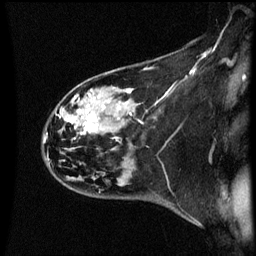
Breast MRI (dynamic contrast-enhanced), one sagittal slice; position 41 of 60 along the scan axis; dynamic contrast-enhanced series, image 2 of 3 at this slice position (ordered by acquisition); 1.5 T; TE 4.2 ms, TR 8.9 ms; 2 mm slice thickness; 256 × 256 image matrix. Female patient, age 44 years. Case-level facts recorded for this patient, not image findings: setting: breast cancer imaged before/during neoadjuvant chemotherapy; receptor status: HR-positive, HER2-negative.
Outlined on this slice (semi-automatically segmented with operator editing):
- analysis volume of interest (the breast-tissue region the enhancement analysis was run in; not a lesion): box from (x=43, y=78) to (x=148, y=189) px
- tumour enhancement mask (voxels above the 70 % enhancement threshold inside the analysis volume of interest): (x=83, y=90)–(x=132, y=133)